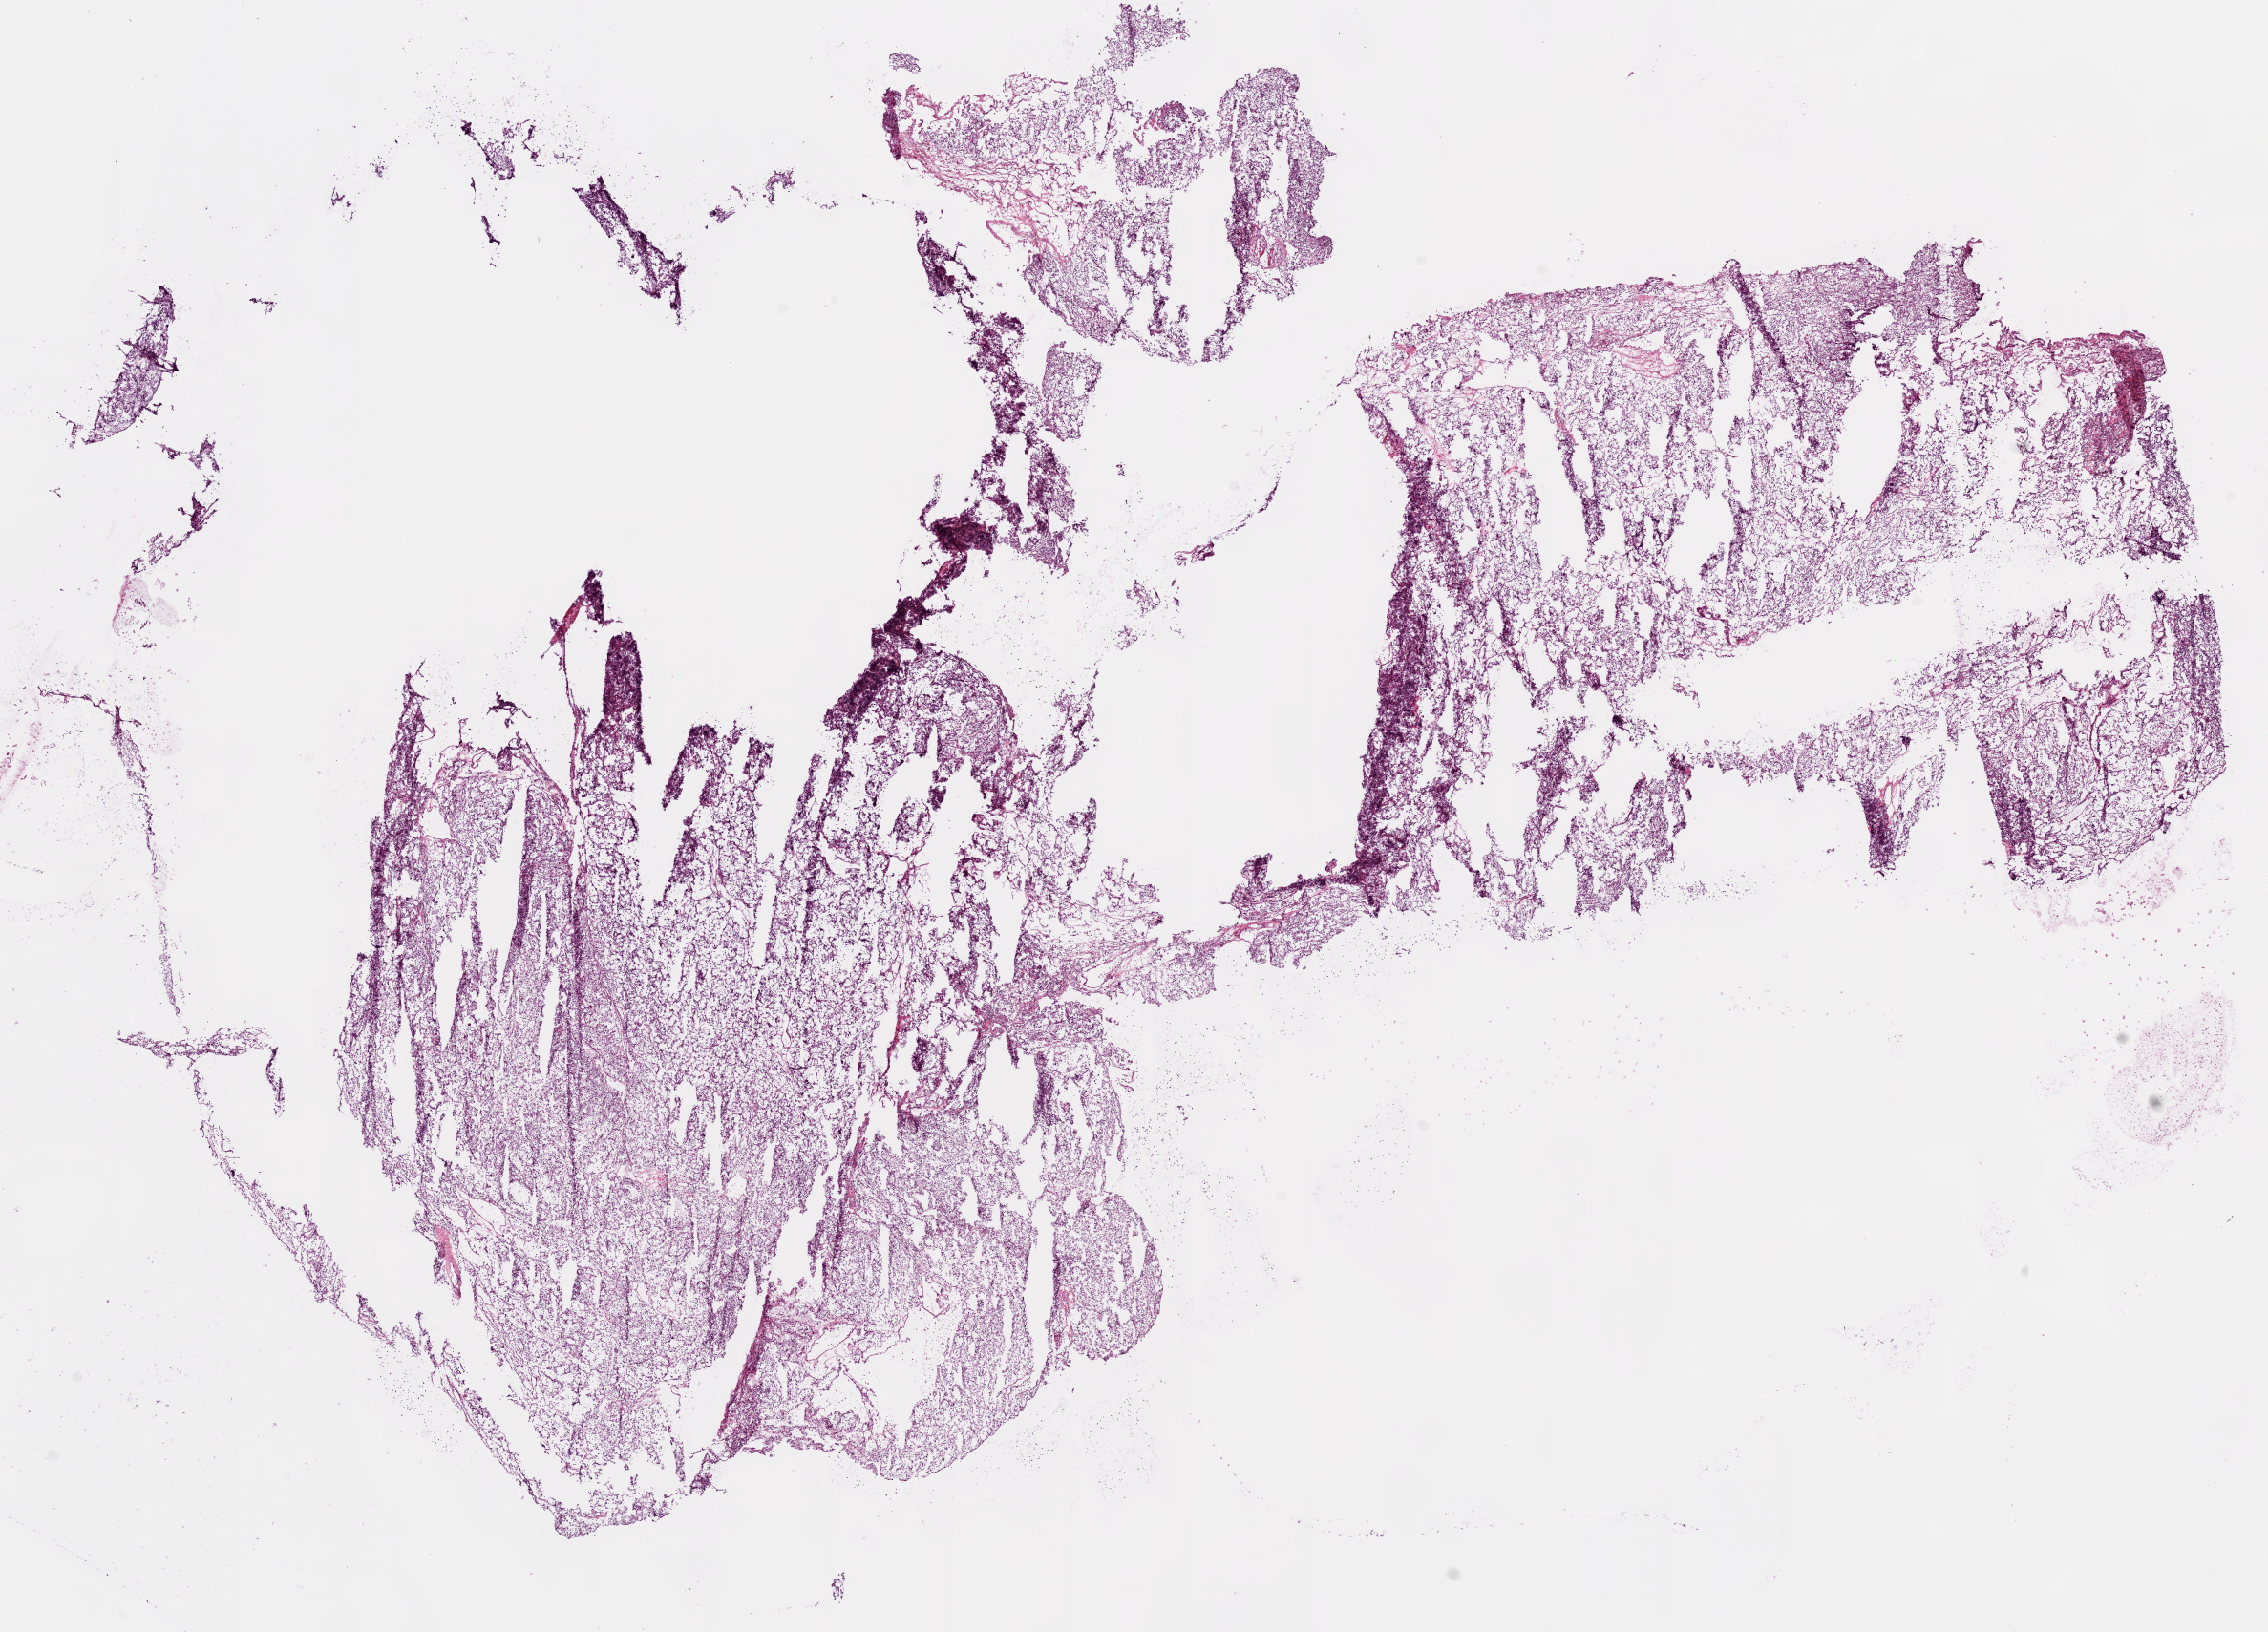
Digitized Hematoxylin and eosin (H&E) stained tissue section (whole slide) — low-resolution overview of the scanned area, about 19.1 x 13.7 mm (from a 20x scan), frozen section from the bottom of the tissue portion, sample: primary tumour, kidney. Female, age 47 years at initial diagnosis. Histologic grade: G2 (moderately differentiated). Pathologist review of this section (percent, as recorded): tumour cells 95%, tumour nuclei 85%, normal cells 0%, stromal cells 5%, necrosis 0%.
* laterality: right
* AJCC pathologic stage: I
* pathologic diagnosis: Clear cell adenocarcinoma, NOS